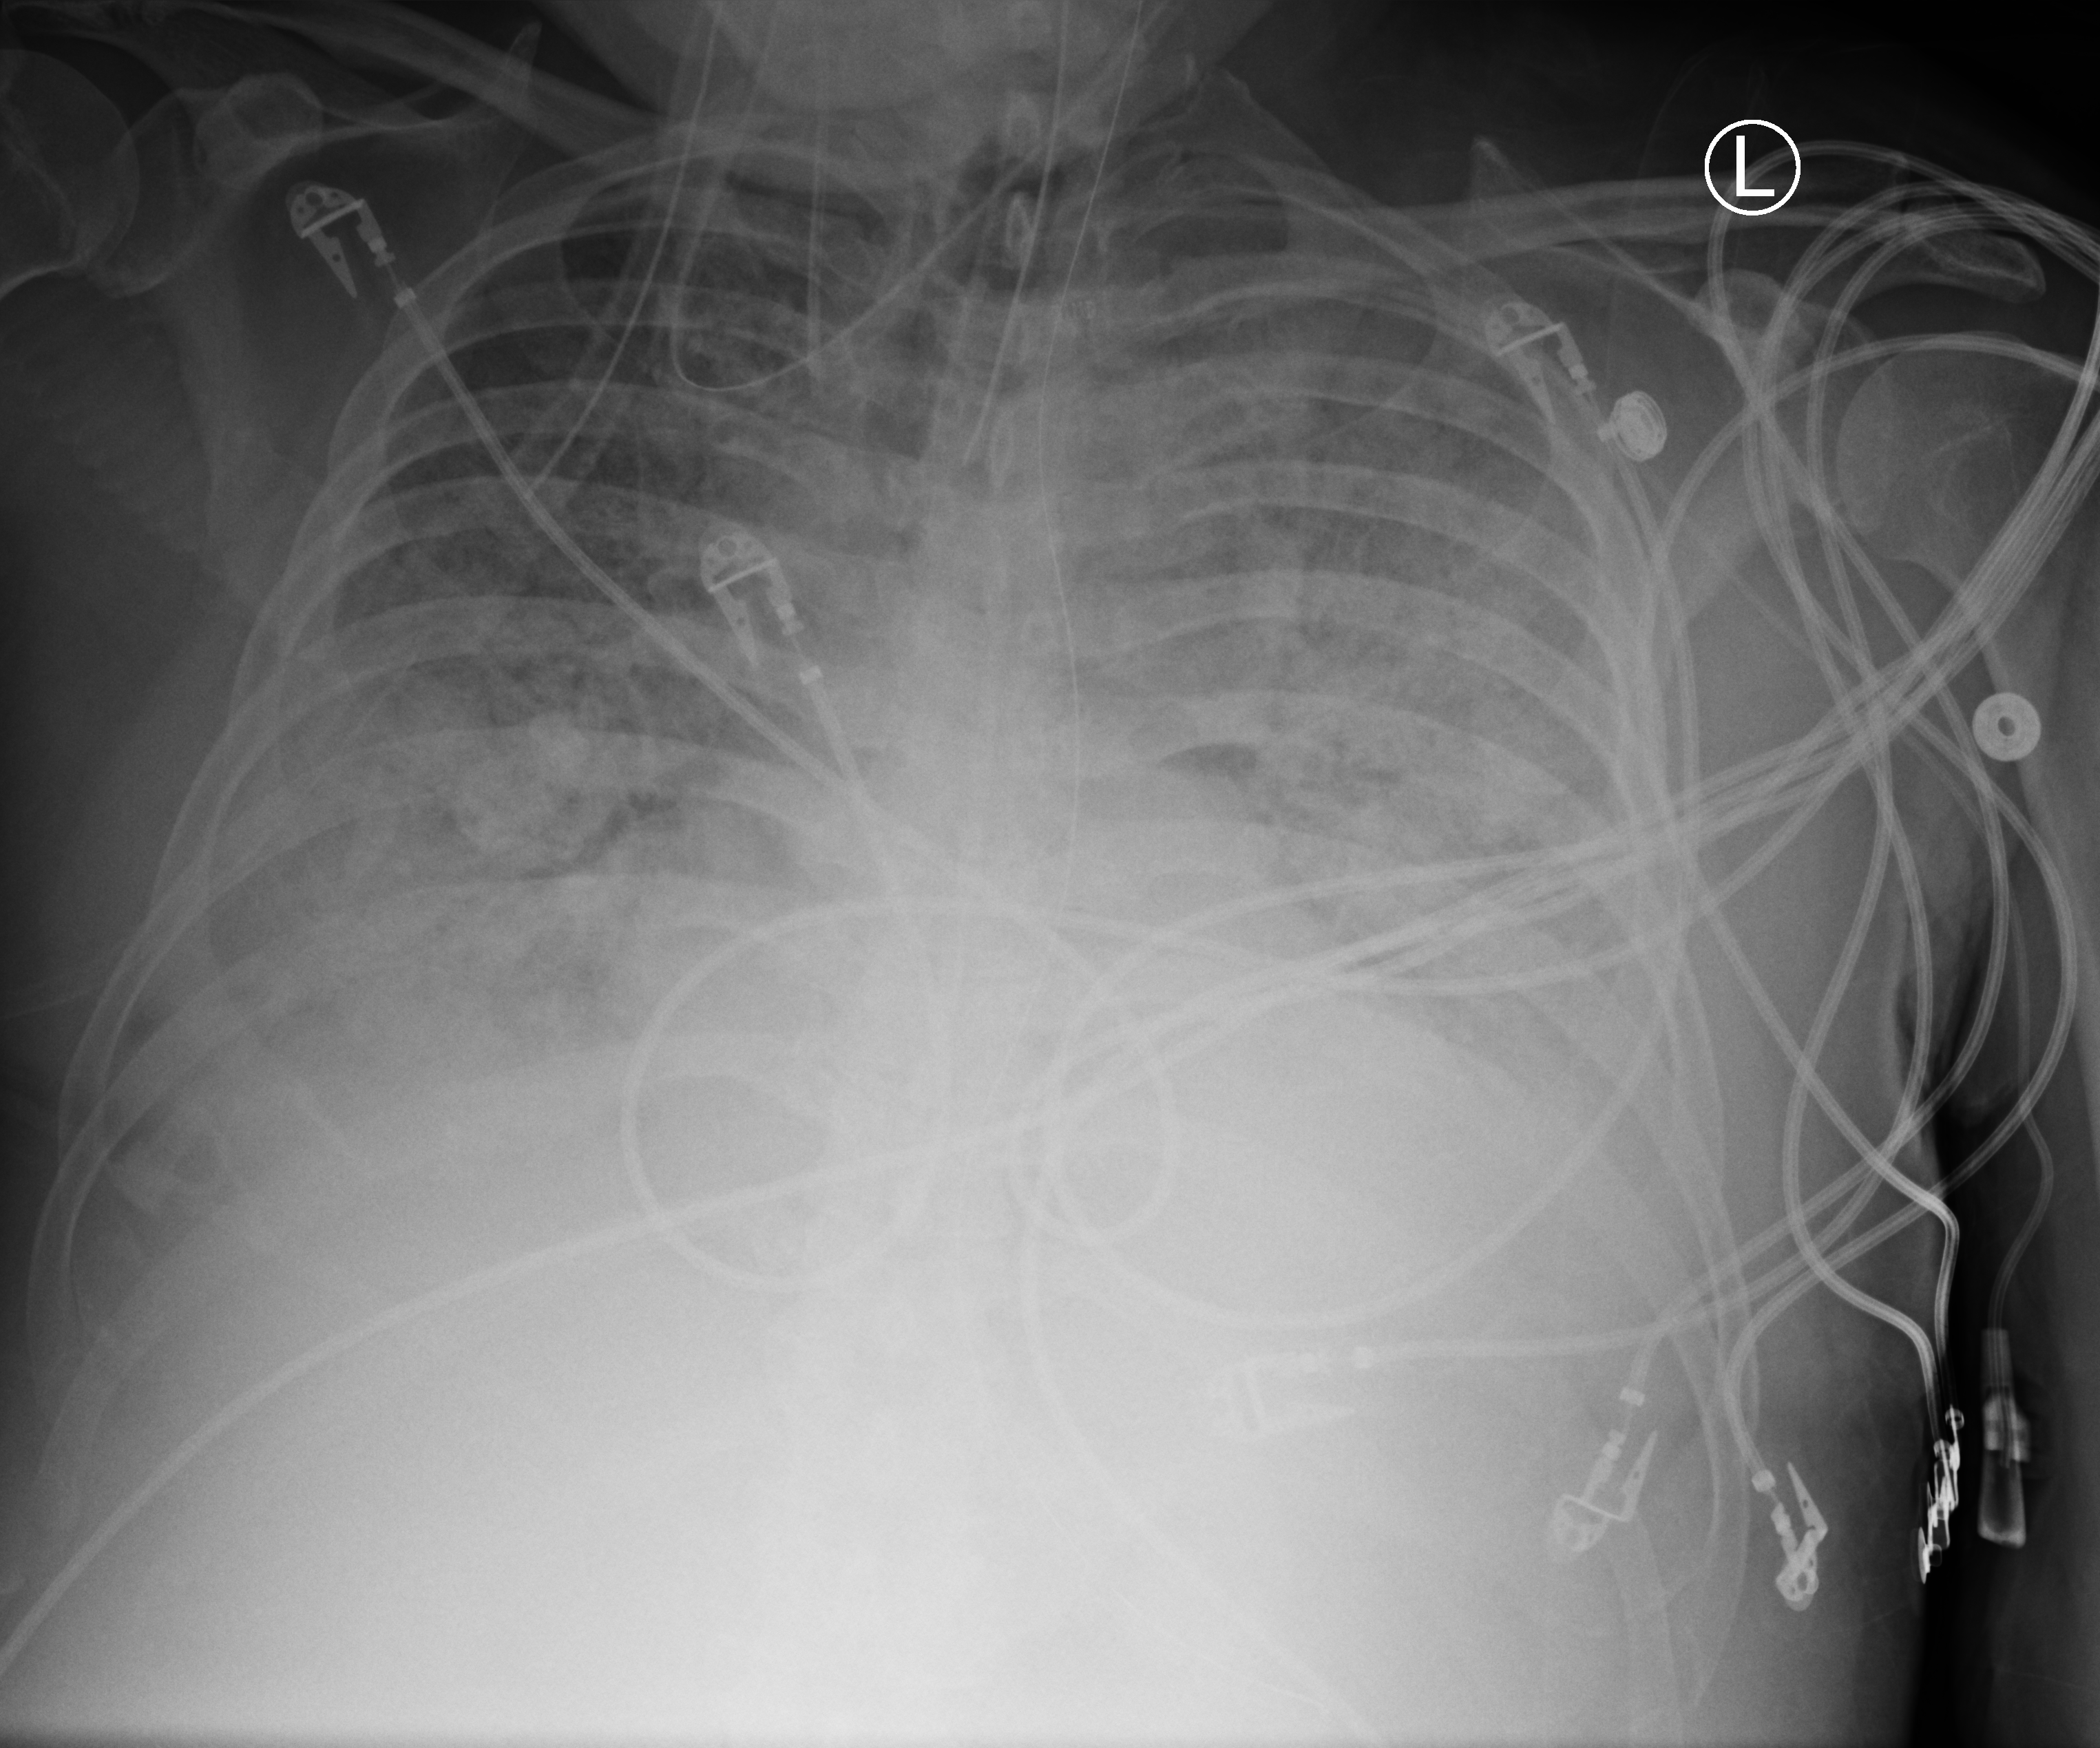
Bedside chest radiograph (computed radiography); anteroposterior (AP) projection. Male patient hospitalised with COVID-19, age 60–74 years.
From the hospital-stay record, not from the radiograph (when in the stay this image was taken is not recorded): mechanically ventilated during this hospital stay: yes; other chronic lung disease (admission record): no.